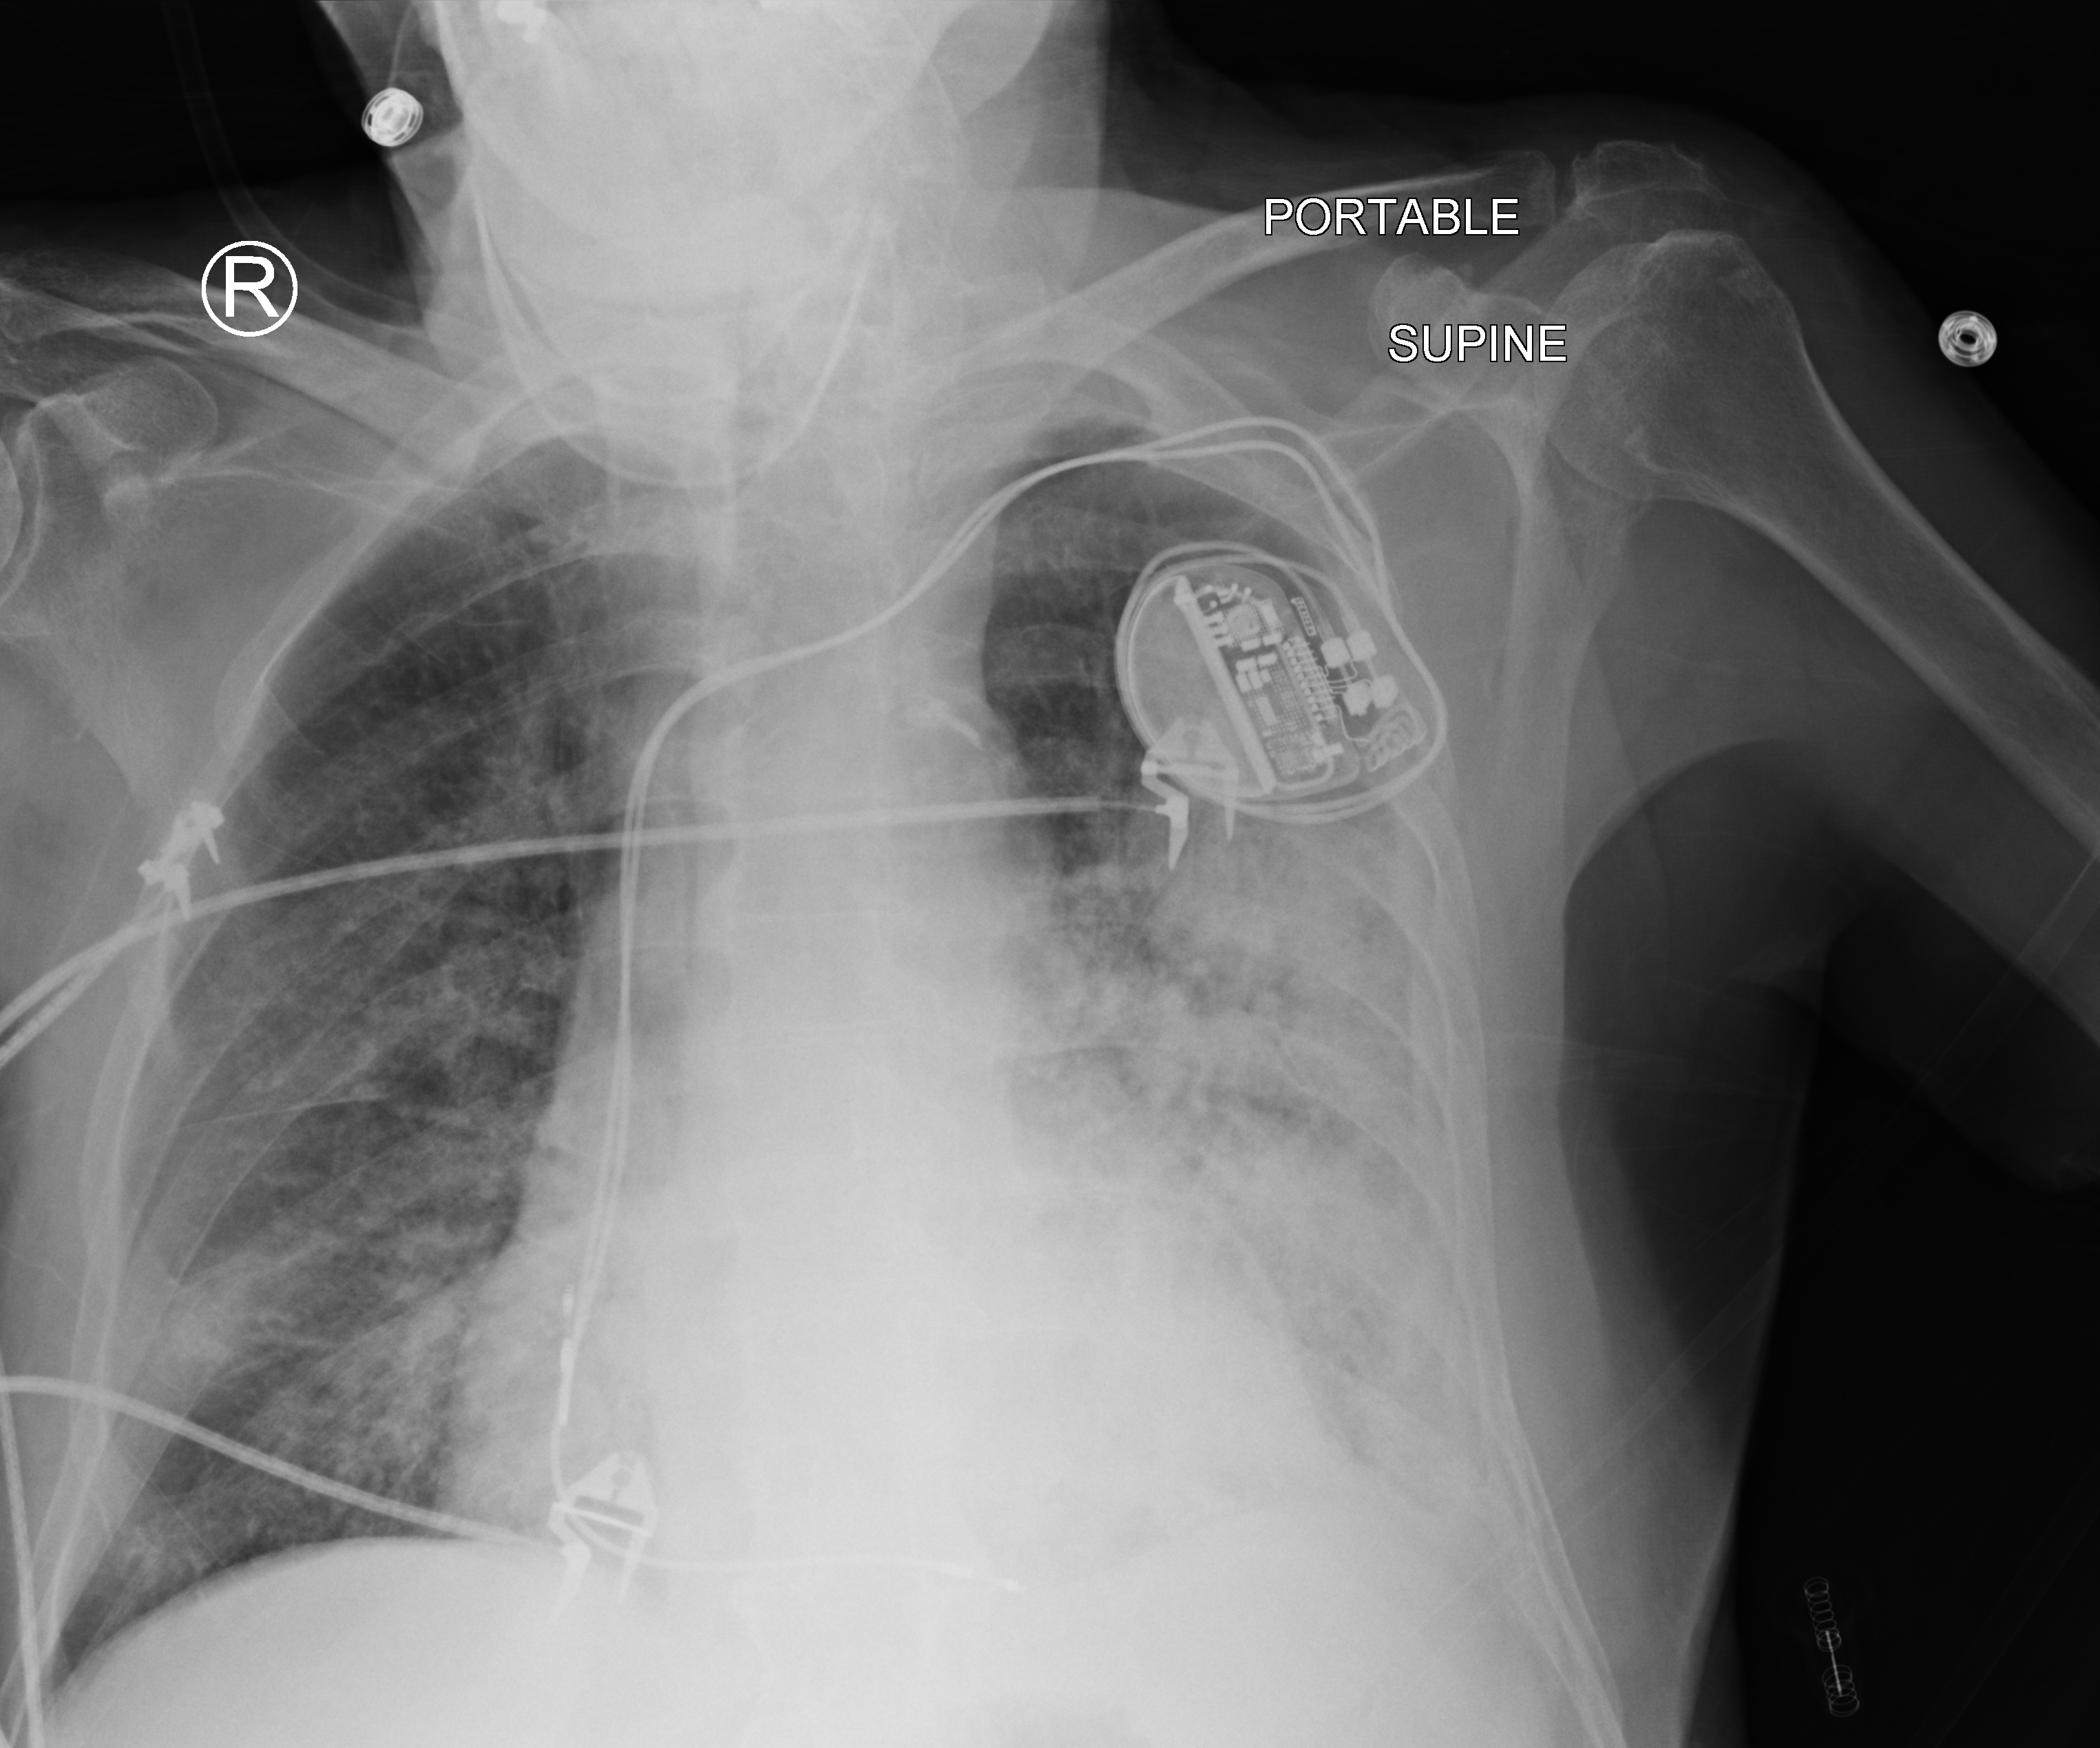
Chest X-ray (portable), anteroposterior (AP) projection. Patient hospitalised with COVID-19; male, aged 75–90 years.
Hospital-stay facts (about this admission, not read from this image; timing relative to this image not recorded): length of hospital stay: 5 days; admitted to intensive care during this hospital stay: no.